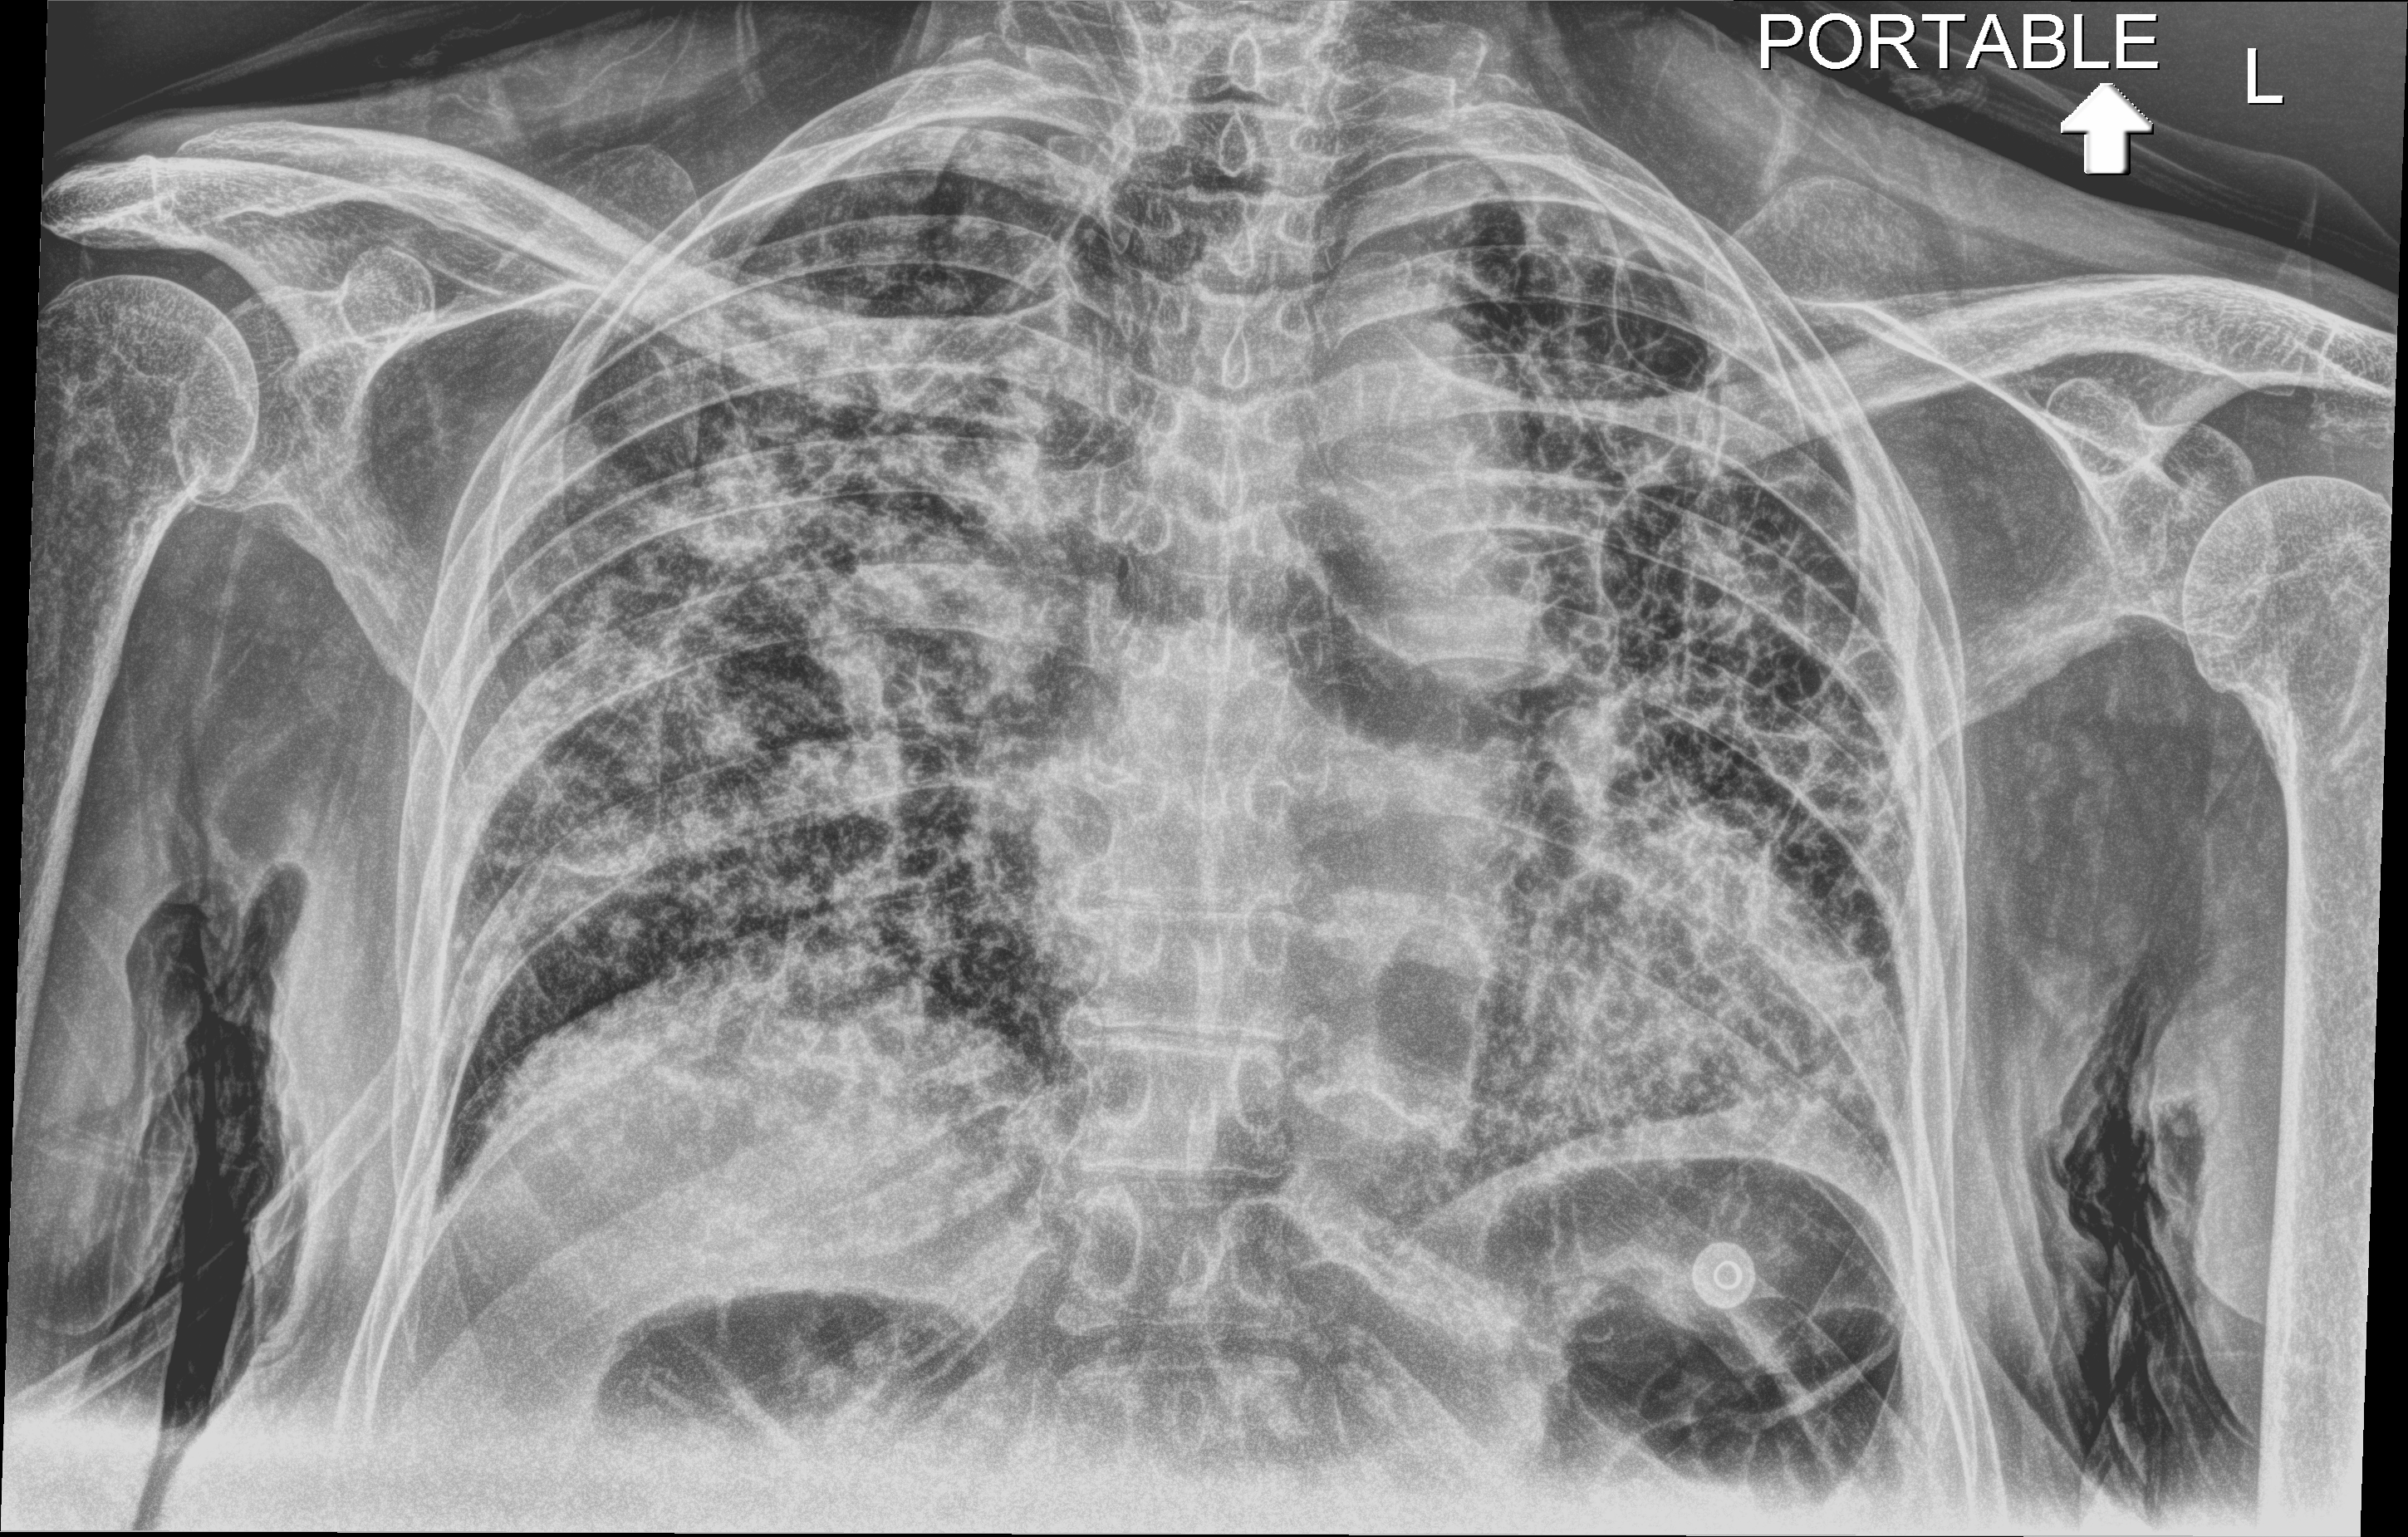
Chest radiograph; anteroposterior (AP) projection. Patient hospitalised with COVID-19; female, aged 60–74 years.
Admission-level facts for this patient (not findings on this image; timing relative to this image not recorded):
- diabetes (admission record): no
- other chronic lung disease (admission record): yes